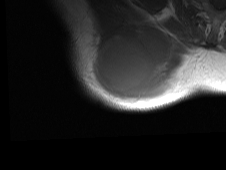
MRI of an extremity soft-tissue mass, one axial slice; position 56 of 81 along the scan axis; MR volume resampled by the dataset authors to the PET/CT grid (not the native acquisition matrix); 3.27 mm slice thickness; 226 × 170 image matrix, field of view 221 × 166 mm. Male patient. From the clinical record (not read from this slice): histological type: pleiomorphic spindle cell undifferentiated; grade: high; site of the primary tumour: right parascapusular.
Annotated regions visible in this slice (expert contour drawn on MRI and transferred to this co-registered scan by the dataset authors):
- gross tumour volume including surrounding oedema: bounding box <90,31,196,105> (left, top, right, bottom; pixels)
- gross tumour volume (mass): <96,36,170,103>